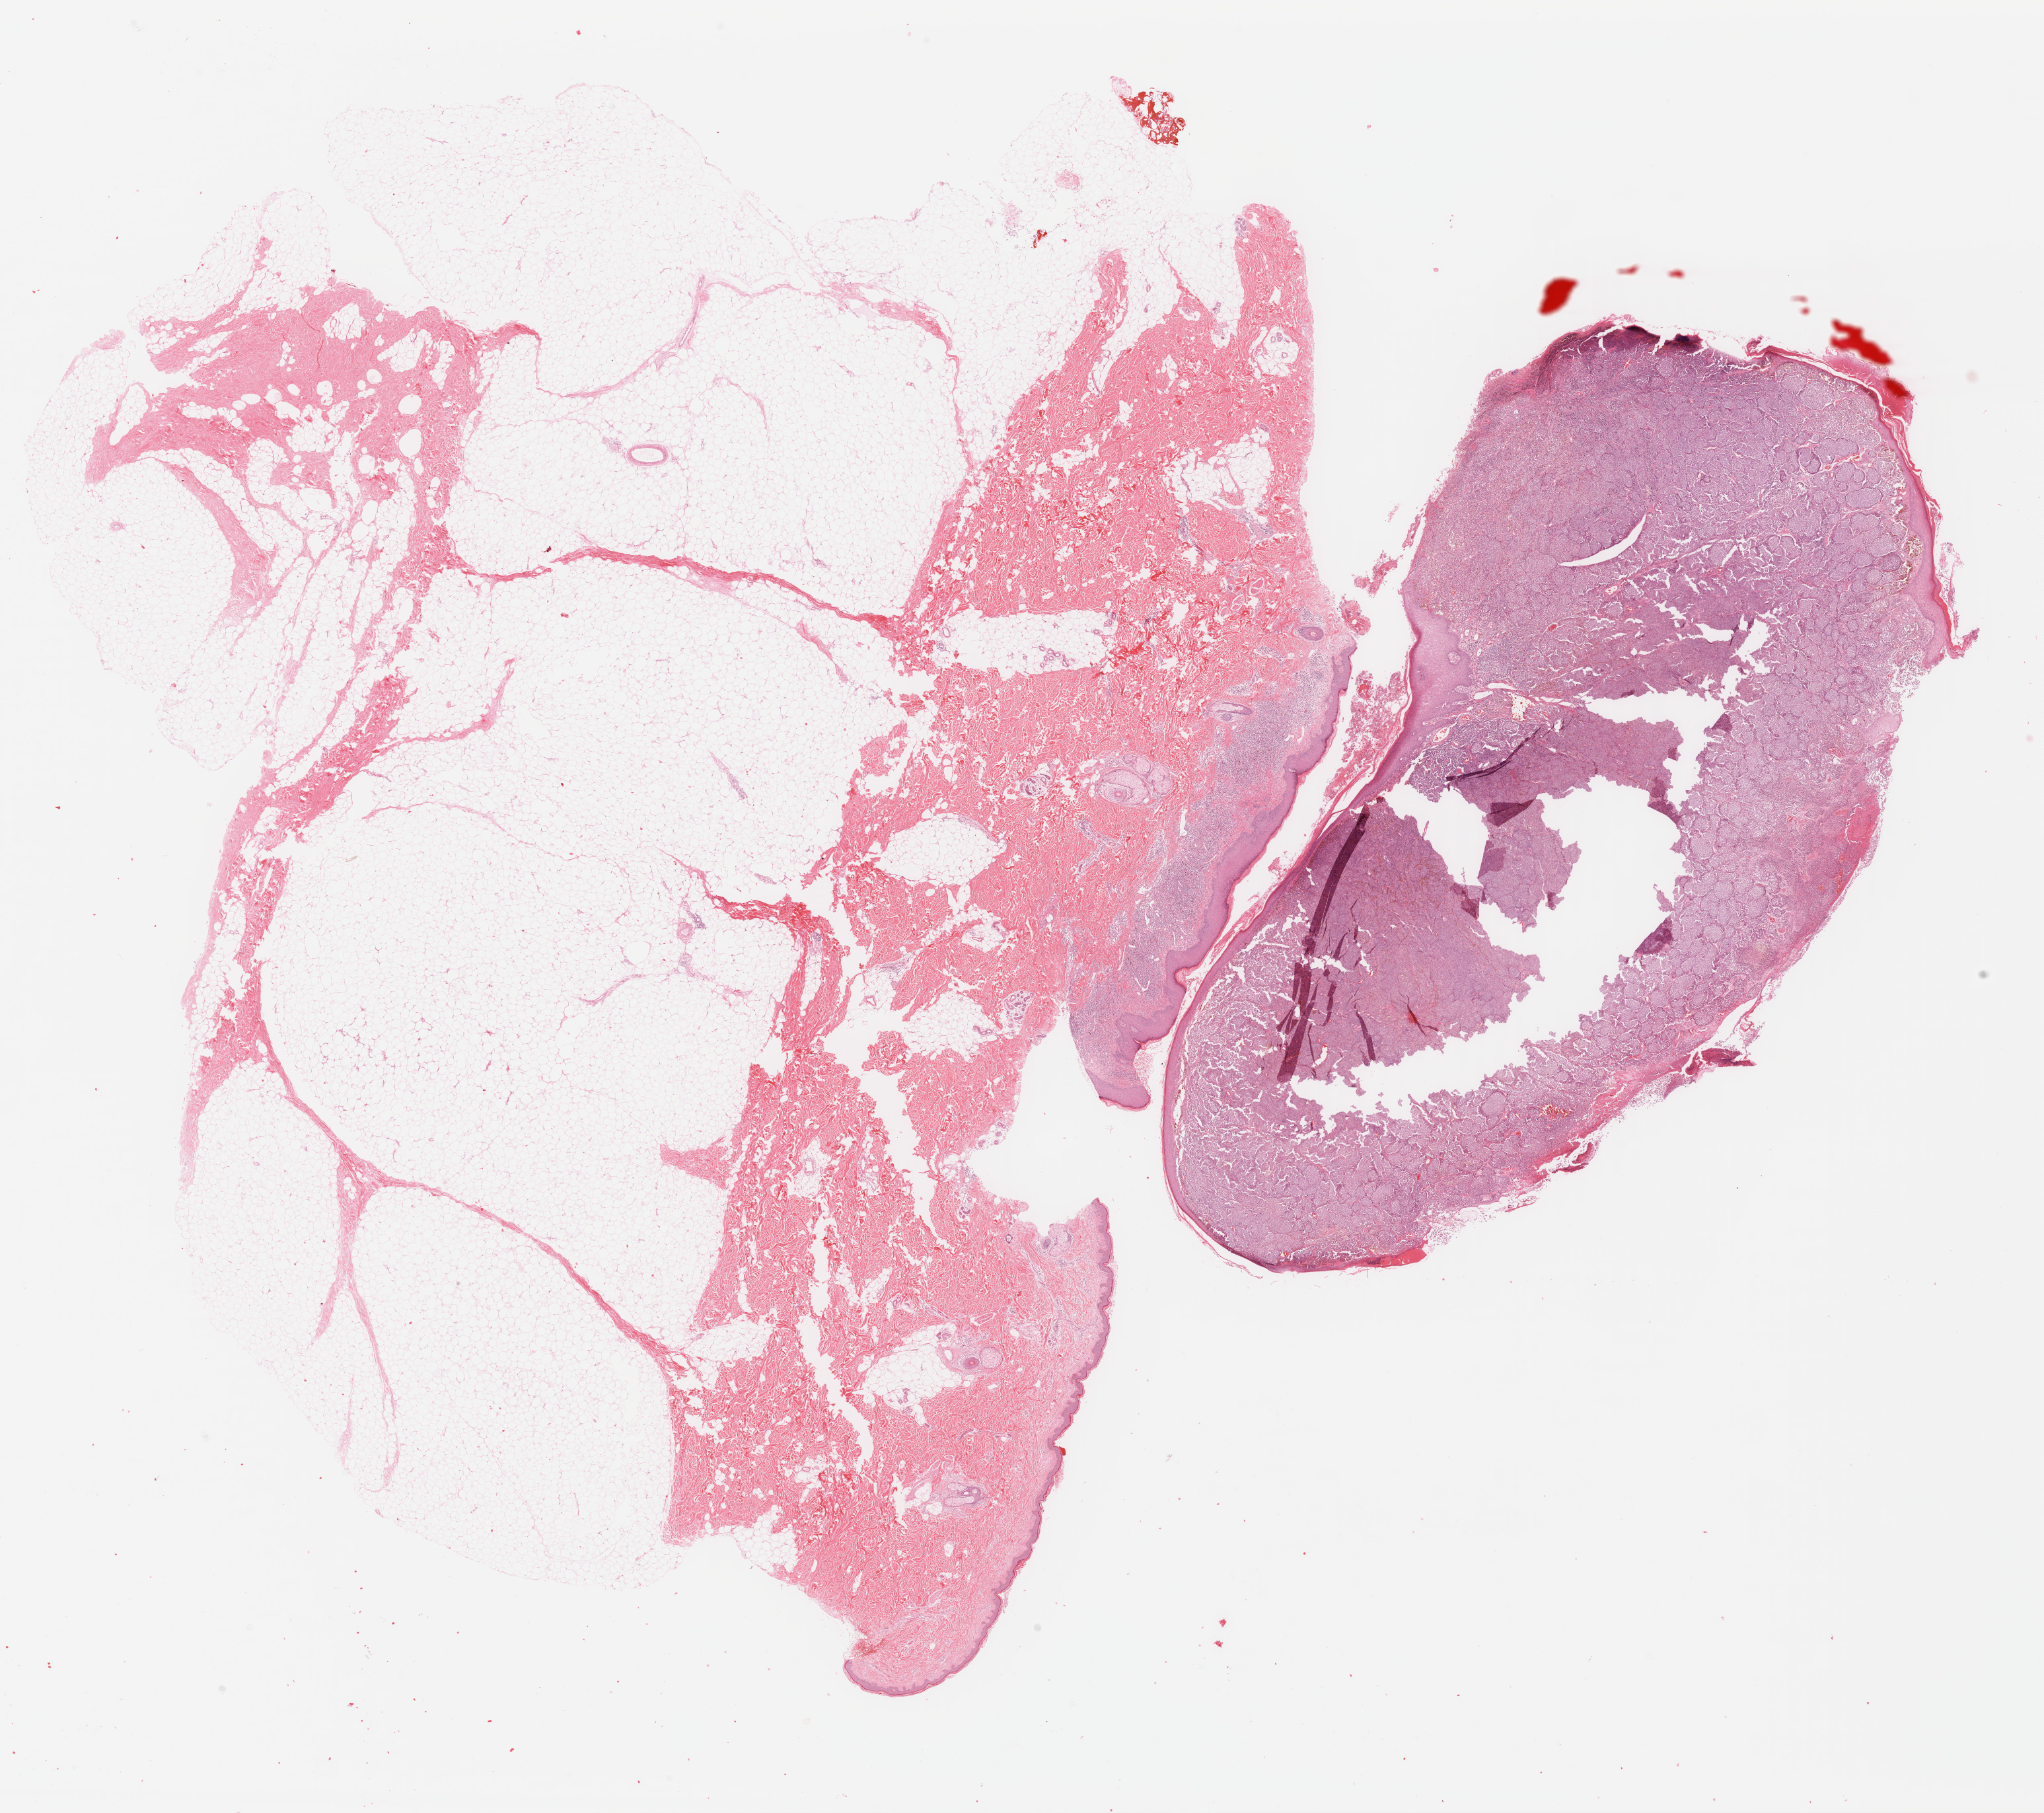
Whole-slide histology image, H&E-stained, shown as a low-resolution overview of the whole scanned area (about 24.3 x 21.6 mm); FFPE section; primary tumour sample from the skin. Female patient; age at initial diagnosis 58 years.
- AJCC pathologic stage: IIC (7th edition)
- diagnosis: Malignant melanoma, NOS